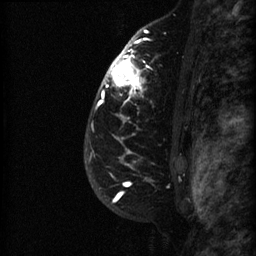
Breast MRI (dynamic contrast-enhanced), one sagittal slice; dynamic contrast-enhanced series, image 2 of 3 at this slice position (ordered by acquisition); 1.5 T; TE 4.2 ms, TR 22.7 ms; 1.5 mm slice thickness; 256 × 256 image matrix, field of view 180 × 180 mm. Female patient, age 48 years. Case-level facts recorded for this patient, not image findings: setting: breast cancer imaged before/during neoadjuvant chemotherapy; receptor status: triple-negative.
Structures marked on this image (semi-automatic segmentation, software-assisted and operator-edited):
- analysis volume of interest (the breast-tissue region the enhancement analysis was run in; not a lesion): box from (x=89, y=27) to (x=191, y=180) px
- tumour enhancement mask (voxels above the 90 % enhancement threshold inside the analysis volume of interest): (x=91, y=30)–(x=151, y=153)